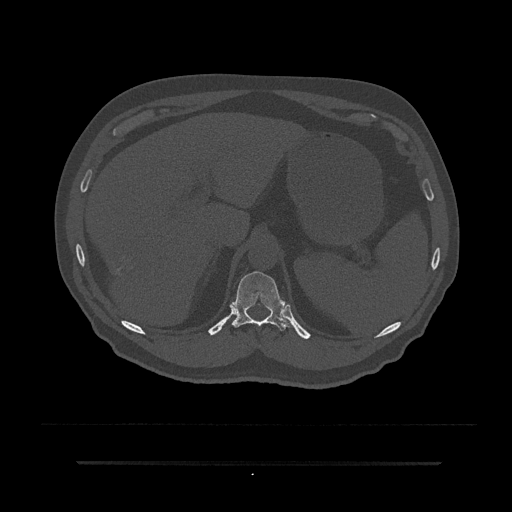
CT including the spine, one axial slice; slice 273 of 797 in the series (ordered by position); reconstruction kernel Br40s/3; 120 kVp; bone window (W 1800 / L 400 HU); 0.5 mm slice thickness; 512 × 512 image matrix, field of view 464 × 464 mm. Male patient, age 59 years. From the clinical record (not read from this slice): primary cancer: bile ducts; vertebrae with lytic lesions (as recorded): T10.
Outlined on this slice (semi-automatic segmentation, software-assisted and operator-edited):
- T11 vertebra: bounding box [x1, y1, x2, y2] px = [231, 271, 293, 331]